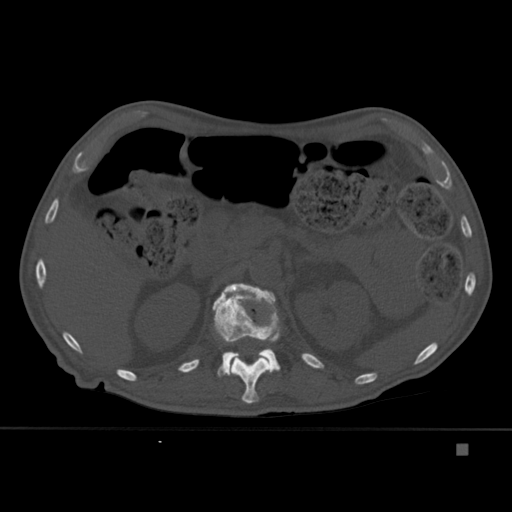
CT including the spine, one axial slice; position 192 of 451 along the scan axis; bone window (W 1800 / L 400 HU); 1.5 mm slice thickness; 512 × 512 image matrix. Male patient, age 75 years. From the clinical record (not read from this slice): primary cancer: prostate.
Structures marked on this image (semi-automatic segmentation, software-assisted and operator-edited):
- L1 vertebra: bounding box (x1, y1, x2, y2) in pixels: (212, 283, 281, 377)
- T12 vertebra: (230, 354, 270, 404)